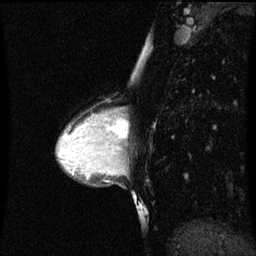
Breast MRI (dynamic contrast-enhanced), one sagittal slice; position 33 of 60 along the scan axis; dynamic contrast-enhanced series, image 2 of 3 at this slice position (ordered by acquisition); 1.5 T; TE 4.2 ms, TR 8.9 ms; 2 mm slice thickness; 256 × 256 image matrix, field of view 200 × 200 mm. Patient: female, 33 years. From the clinical record (not read from this slice): setting: breast cancer imaged before/during neoadjuvant chemotherapy; receptor status: HER2-positive.
Outlined on this slice (semi-automatic segmentation, software-assisted and operator-edited):
- analysis volume of interest (the breast-tissue region the enhancement analysis was run in; not a lesion): bounding box (x1, y1, x2, y2) in pixels: (107, 108, 122, 147)
- tumour enhancement mask (voxels above the 70 % enhancement threshold inside the analysis volume of interest): (109, 118, 121, 141)